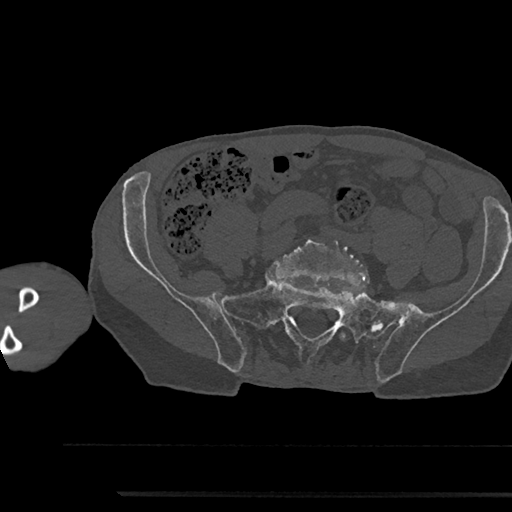
CT including the spine, one axial slice. Position 309 of 797 along the scan axis. Reconstruction kernel Br40s/3. 120 kVp. Bone window (W 1800 / L 400 HU). 0.5 mm slice thickness. 512 × 512 image matrix. Male patient, age 79 years. From the clinical record (not read from this slice): primary cancer: prostate.
Annotated regions visible in this slice (semi-automatically segmented with operator editing):
- L5 vertebra: box from (x=274, y=234) to (x=369, y=340) px